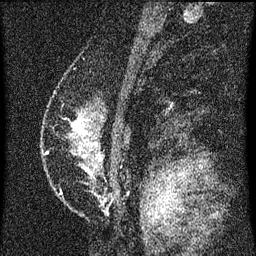
Breast MRI (dynamic contrast-enhanced), one sagittal slice; position 41 of 60 along the scan axis; dynamic contrast-enhanced series, image 2 of 3 at this slice position (ordered by acquisition); 1.5 T; TE 4.2 ms, TR 8 ms; 2 mm slice thickness; 256 × 256 image matrix, field of view 180 × 180 mm. Patient: female, 47 years.
Structures marked on this image (semi-automatically segmented with operator editing):
- analysis volume of interest (the breast-tissue region the enhancement analysis was run in; not a lesion): bounding box <61,86,128,203> (left, top, right, bottom; pixels)
- tumour enhancement mask (voxels above the 70 % enhancement threshold inside the analysis volume of interest): <73,122,81,131>